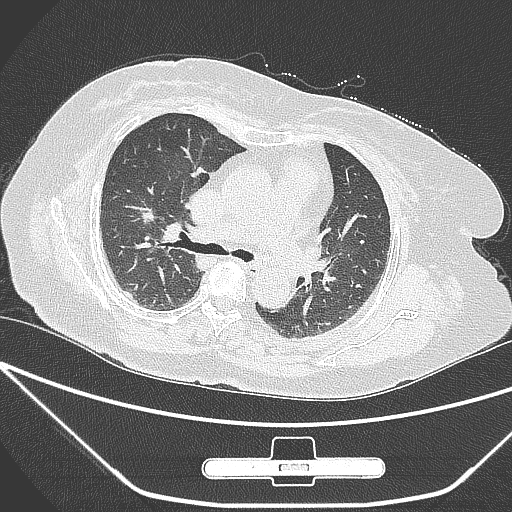
Chest CT, one axial slice; position 166 of 245 along the scan axis; 120 kVp; lung window (W 1500 / L -600 HU); 512 × 512 image matrix, field of view 365 × 365 mm. Female patient, age 65 years. Case-level facts recorded for this patient, not image findings: clinical TNM (as recorded): T1c N0 M0; histopathological grade: G3.
Structures marked on this image (rectangle marked by the reading radiologist):
- lung tumour (recorded histology: adenocarcinoma): bounding box (x1, y1, x2, y2) in pixels: (132, 200, 160, 233)